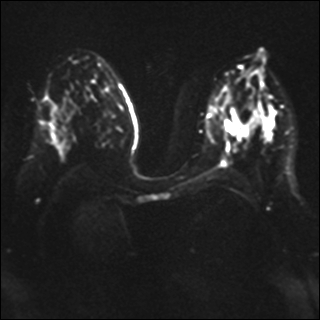
Breast MRI, one axial slice. Position 20 of 37 along the scan axis. Diffusion-weighted series; image 2 of 4 stored at this slice position (different b-values; order by instance number). 1.5 T. 4 mm slice thickness. 320 × 320 image matrix, field of view 340 × 340 mm. Female patient.
Annotated regions visible in this slice (outlined manually by an expert reader):
- tumour on diffusion-weighted imaging: bounding box <232,122,251,136> (left, top, right, bottom; pixels)